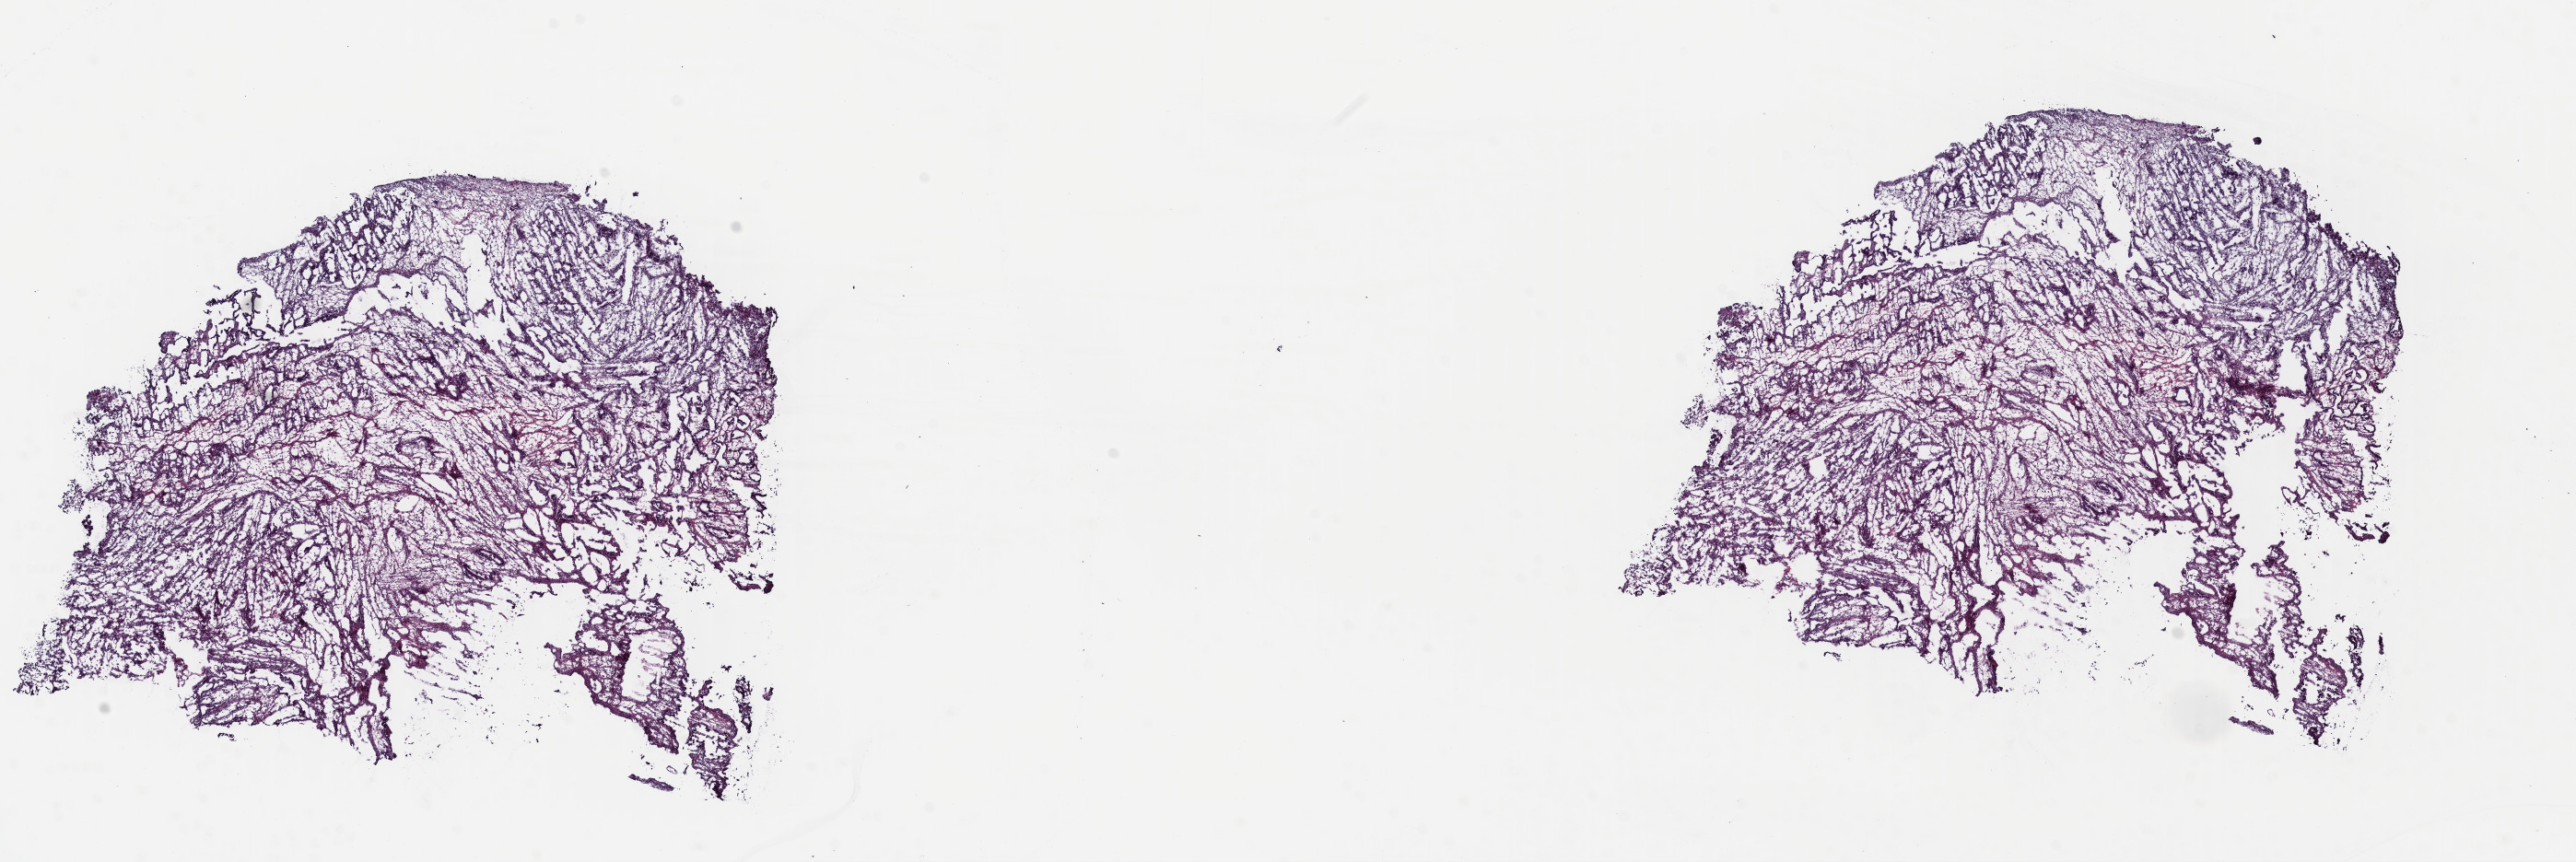
Digitized Hematoxylin and eosin (H&E) stained tissue section (whole slide) — a low-resolution overview of the entire scanned area, about 22.0 x 7.4 mm (acquisition: 40x scan); frozen section from the top of the tissue portion; uterus, primary tumour sample. Female patient; age at initial diagnosis 65 years. Pathologist review of this section (percent, as recorded): tumour cells 100%, tumour nuclei 80%, normal cells 0%, stromal cells 0%, necrosis 0%. Inflammatory infiltration, as recorded: lymphocyte infiltration 1%, monocyte infiltration 0%, neutrophil infiltration 0%.
FIGO stage: IB. Histologic diagnosis: Mullerian mixed tumor (endometrium).